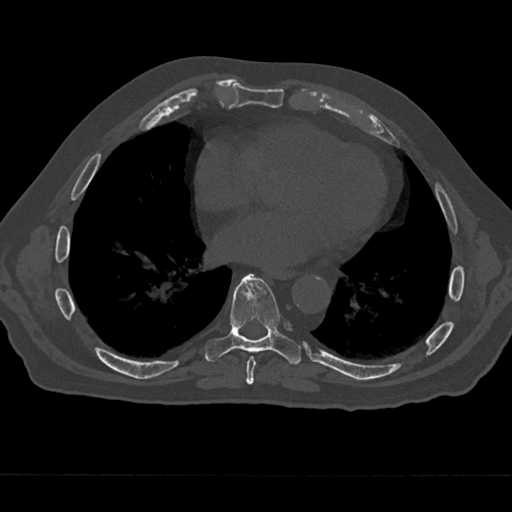
CT including the spine, one axial slice; slice 325 of 797 in the series (ordered by position); reconstruction kernel Br40s/3; 120 kVp; bone window (W 1800 / L 400 HU); 0.5 mm slice thickness; 512 × 512 image matrix. Male patient, age 75 years. From the clinical record (not read from this slice): primary cancer: renal.
Outlined on this slice (semi-automatic segmentation, software-assisted and operator-edited):
- T7 vertebra: box from (x=243, y=356) to (x=258, y=385) px
- T8 vertebra: (x=204, y=273)–(x=301, y=365)